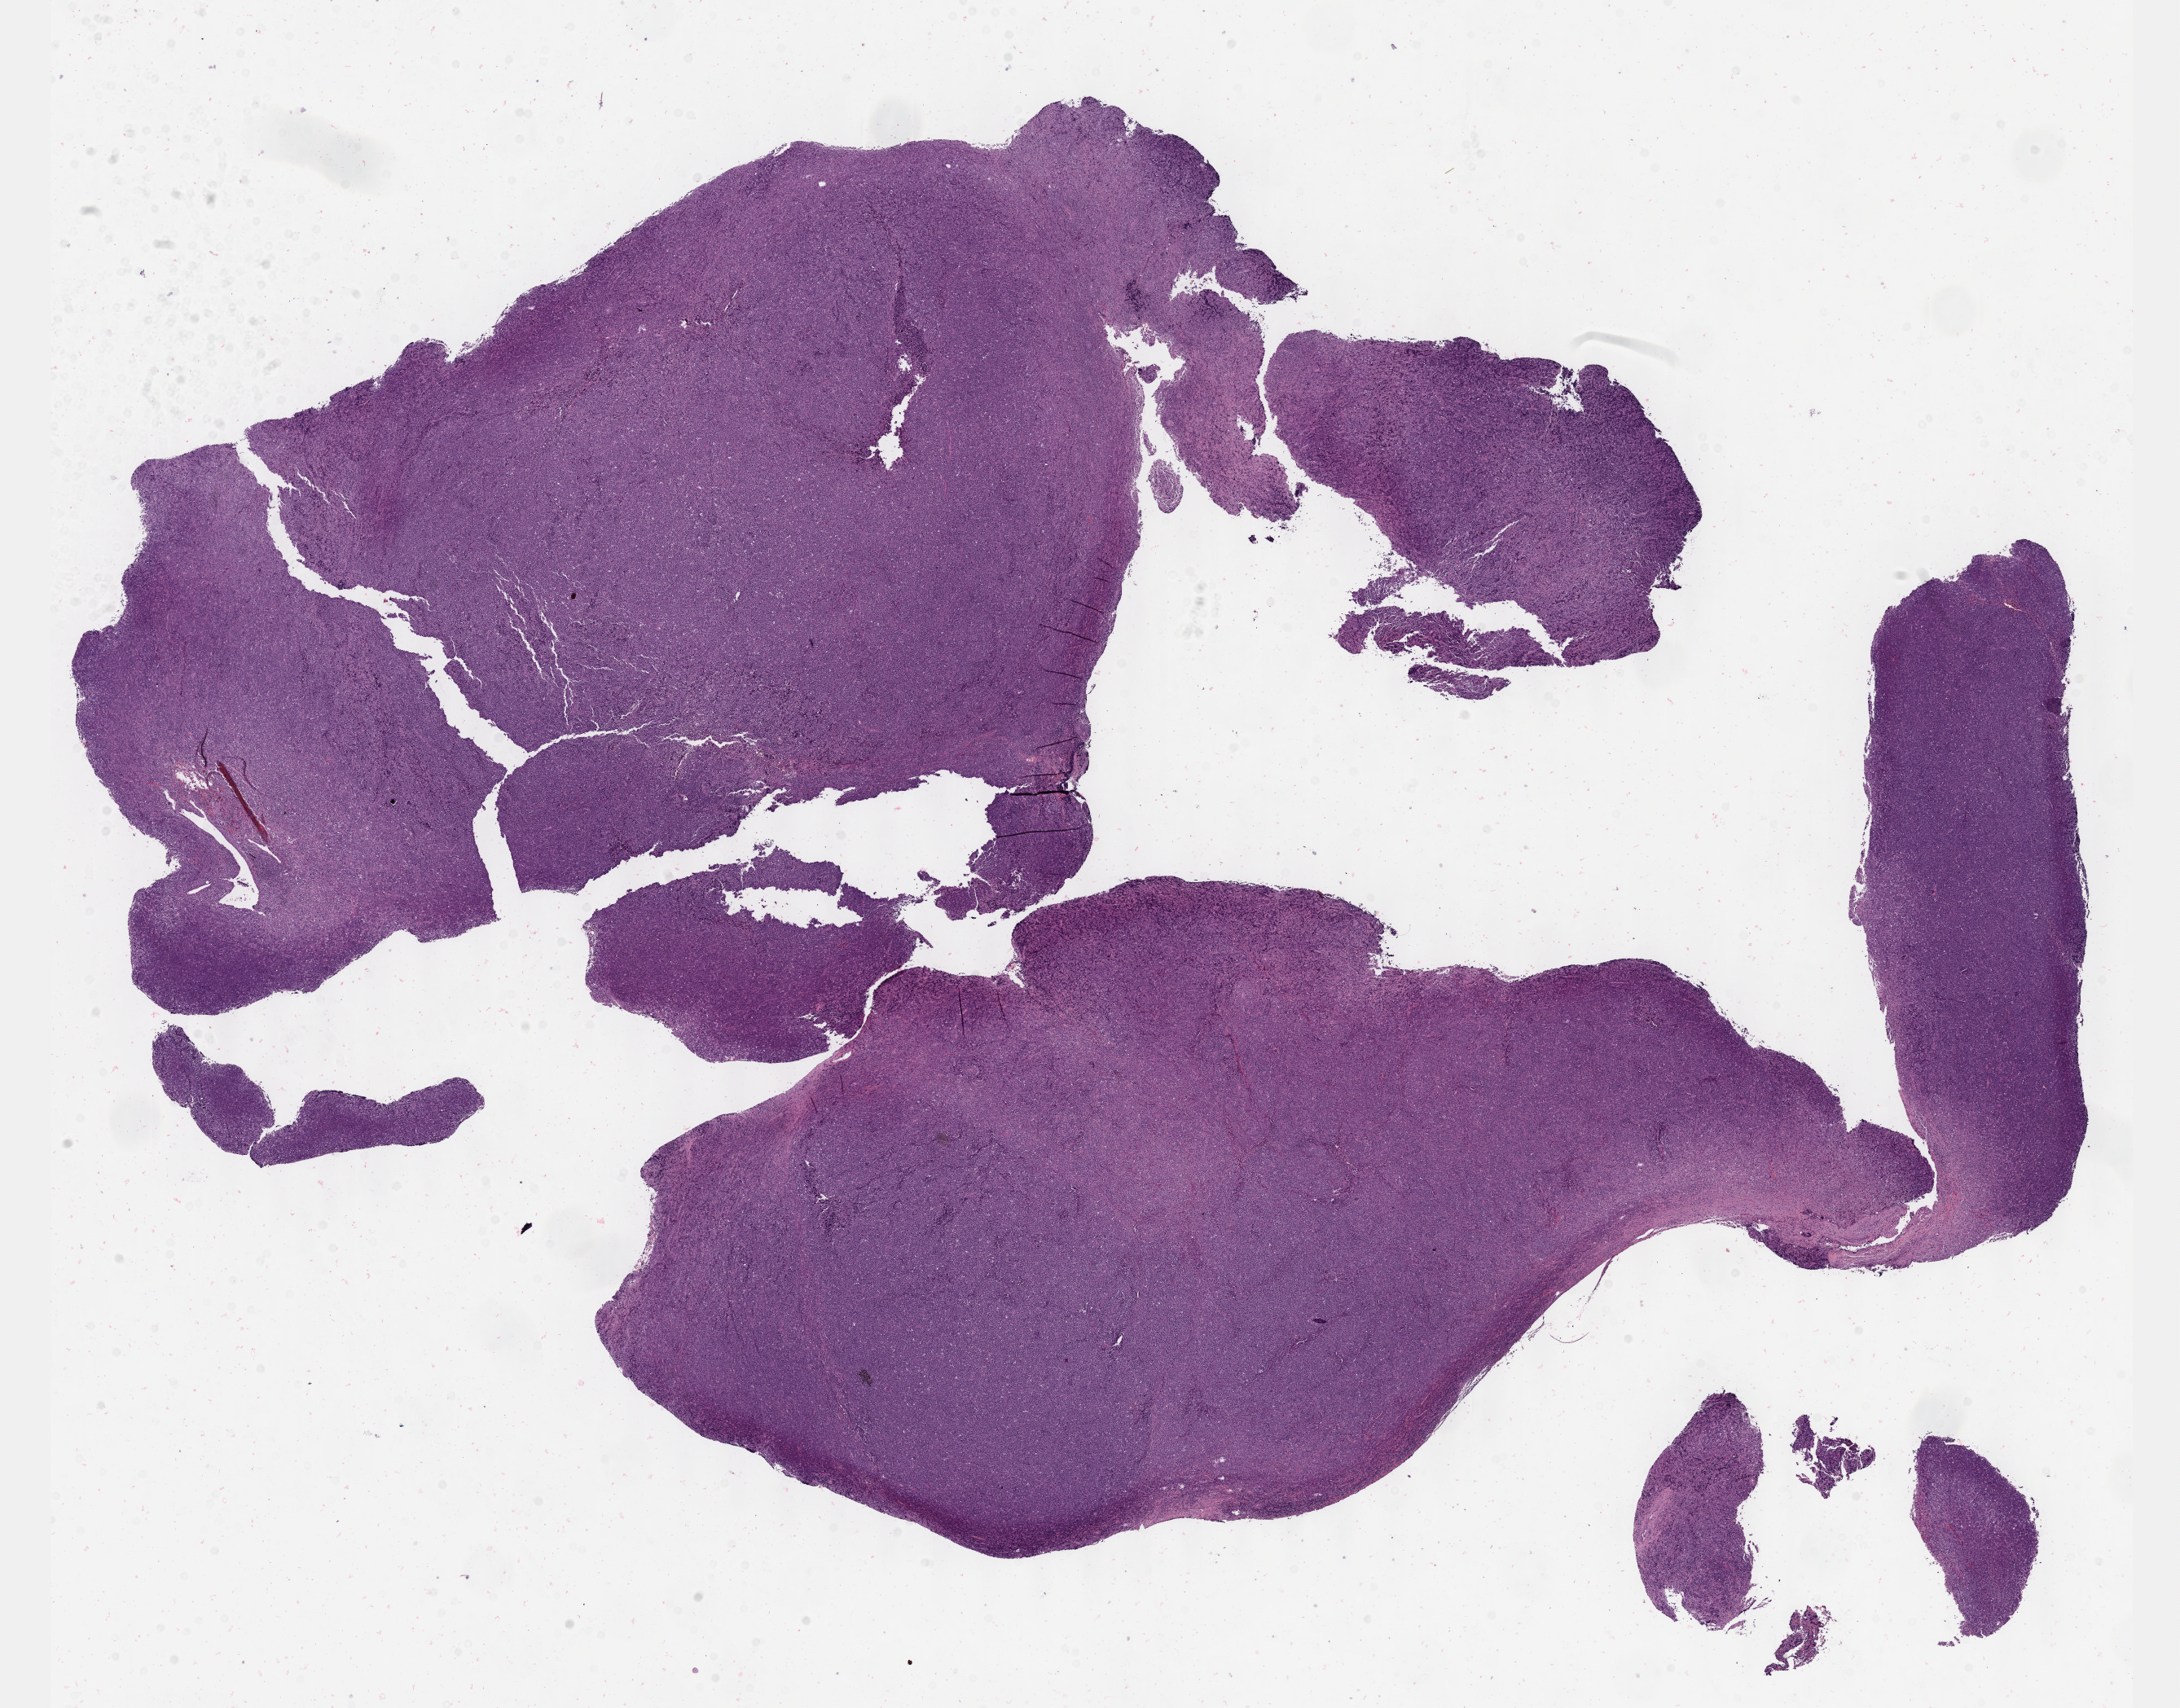
Digitized H&E tissue section (whole slide), a low-resolution overview of the entire scanned area, about 21.6 x 16.9 mm (from a 40x scan). Formalin-fixed paraffin-embedded (FFPE) diagnostic section. Lymphoid tissue, primary tumour sample. Patient: female, age at initial diagnosis 69 years.
Pathologic diagnosis: Diffuse large B-cell lymphoma, NOS (lymph nodes of inguinal region or leg).